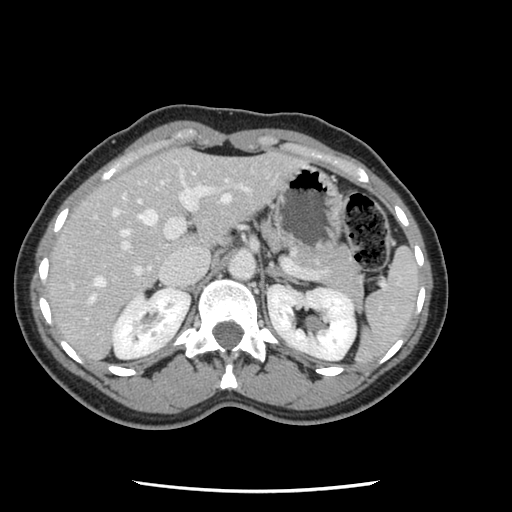
Contrast-enhanced abdominal CT, one axial slice. Soft-tissue window (W 400 / L 40 HU). 2.5 mm slice thickness. 512 × 512 image matrix. Female patient, age 43 years. From the clinical record (not read from this slice): diagnosis: colorectal cancer liver metastases, imaged before liver resection; multiple liver metastases: yes; largest metastasis: 3.4 cm.
Outlined on this slice (manually delineated by an expert):
- hepatic veins: bounding box (x1, y1, x2, y2) in pixels: (89, 182, 229, 303)
- liver: (48, 149, 299, 360)
- planned liver remnant (the part of the liver to remain after resection): (47, 153, 188, 305)
- portal vein (with intrahepatic branches): (71, 170, 251, 298)